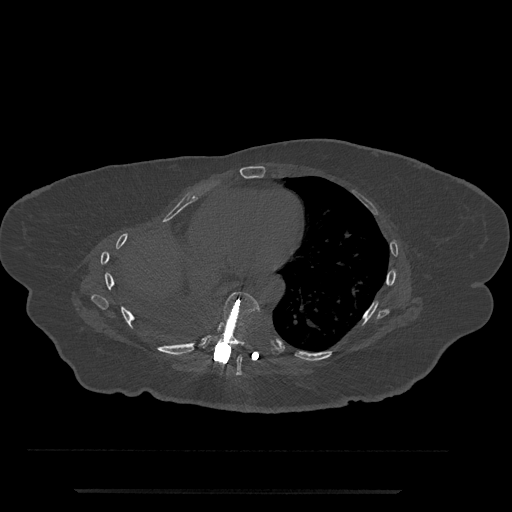
CT including the spine, one axial slice; 120 kVp; bone window (W 1800 / L 400 HU); 0.5 mm slice thickness; 512 × 512 image matrix, field of view 440 × 440 mm. Female patient, age 51 years. From the clinical record (not read from this slice): primary cancer: neuro; vertebrae with lytic lesions (as recorded): T8.
Annotated regions visible in this slice (semi-automatic segmentation, software-assisted and operator-edited):
- T7 vertebra: box from (x=234, y=355) to (x=242, y=376) px
- T8 vertebra: (x=203, y=292)–(x=260, y=352)